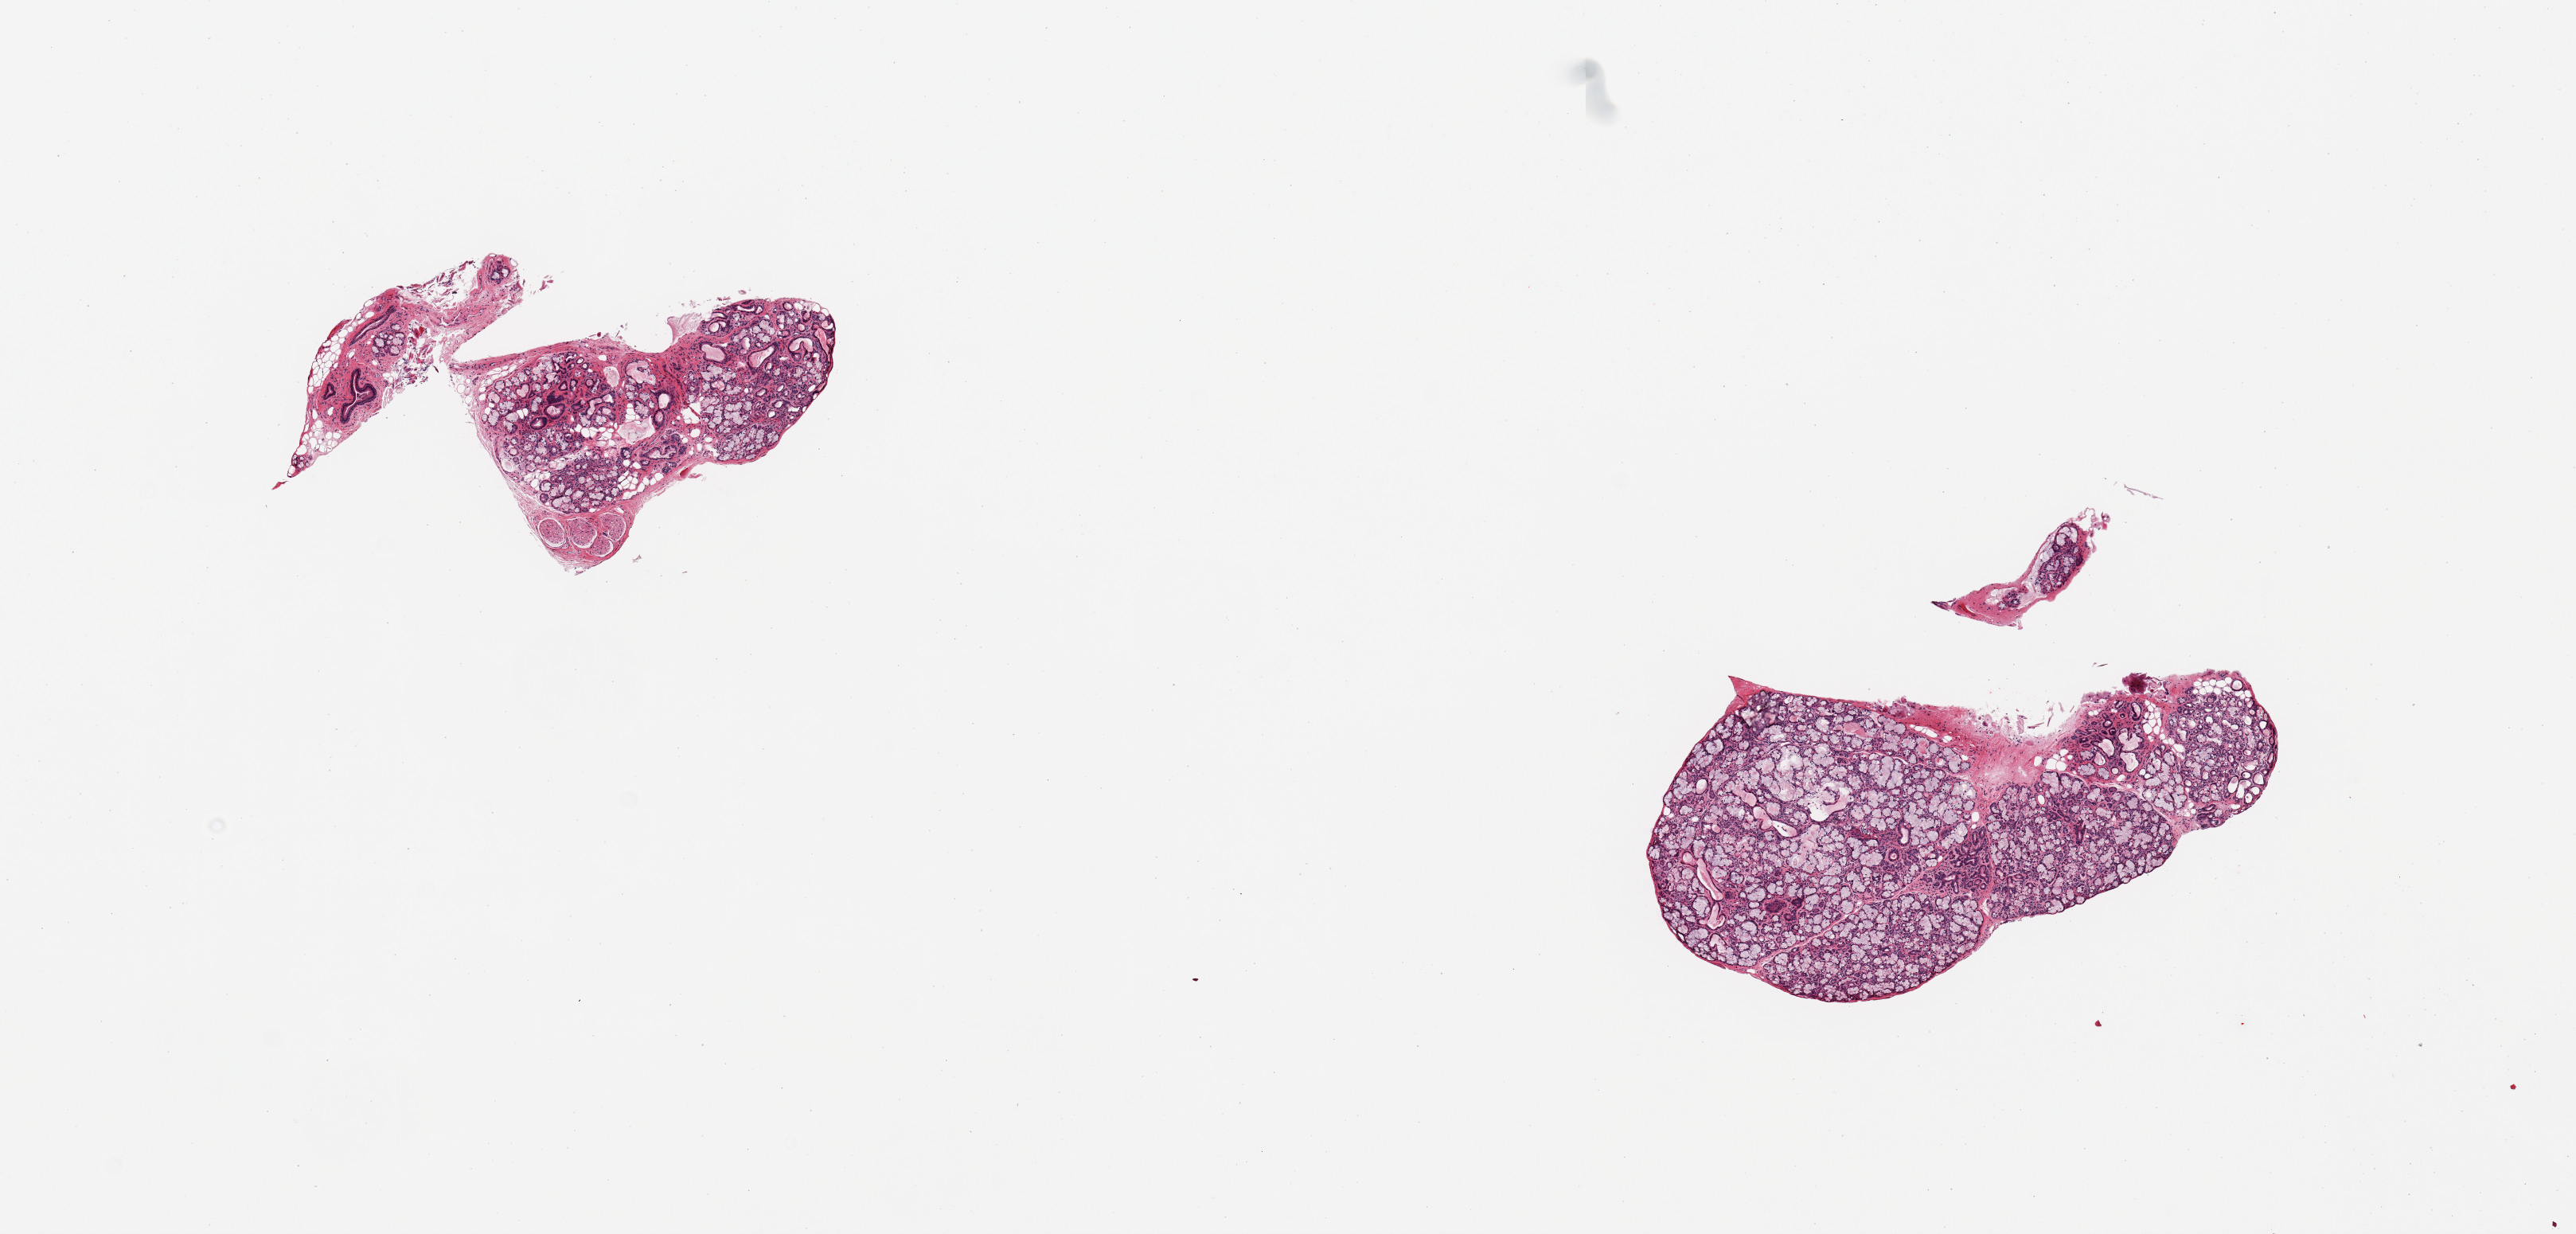
Digitized H&E-stained section, brightfield, whole scanned area (about 12.8 x 6.1 mm, slide scanned at 20x) shown as a low-resolution overview, PAXgene-fixed, paraffin-embedded tissue, sampled site (target tissue): minor salivary gland, tissue donor sample. Donor: male.
Reviewer comment on this tissue sample: 2 pieces, 95% glandular/ductal elements.